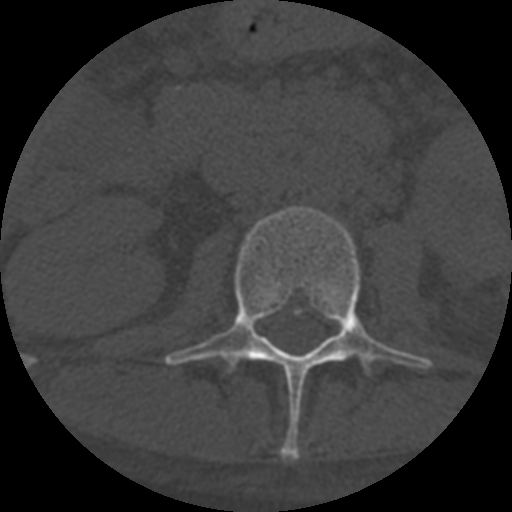
CT including the spine, one axial slice; slice 261 of 708 in the series (ordered by position); reconstruction kernel STANDARD; one of 3 acquisitions stored at this slice position; bone window (W 1800 / L 400 HU); 1.25 mm slice thickness; 512 × 512 image matrix, field of view 160 × 160 mm. Patient age 55 years. From the clinical record (not read from this slice): primary cancer: colon.
Outlined on this slice (semi-automatic segmentation, software-assisted and operator-edited):
- L2 vertebra: box from (x=164, y=206) to (x=433, y=460) px